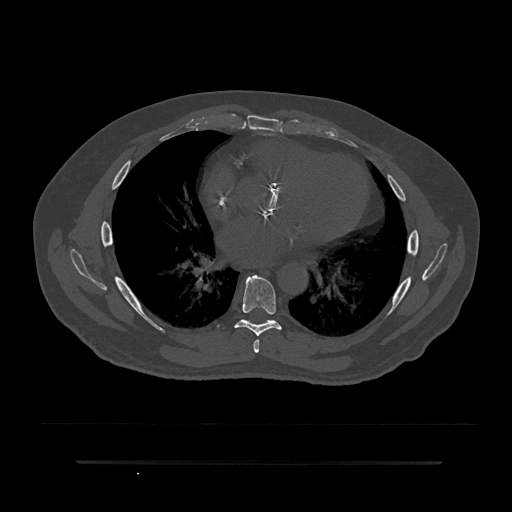
CT including the spine, one axial slice; slice 479 of 797 in the series (ordered by position); 120 kVp; bone window (W 1800 / L 400 HU); 0.5 mm slice thickness; 512 × 512 image matrix, field of view 464 × 464 mm. Patient: male, 59 years. Case-level facts recorded for this patient, not image findings: primary cancer: bile ducts.
Structures marked on this image (semi-automatically segmented with operator editing):
- T6 vertebra: bounding box [x1, y1, x2, y2] px = [253, 339, 260, 353]
- T7 vertebra: [234, 275, 282, 336]